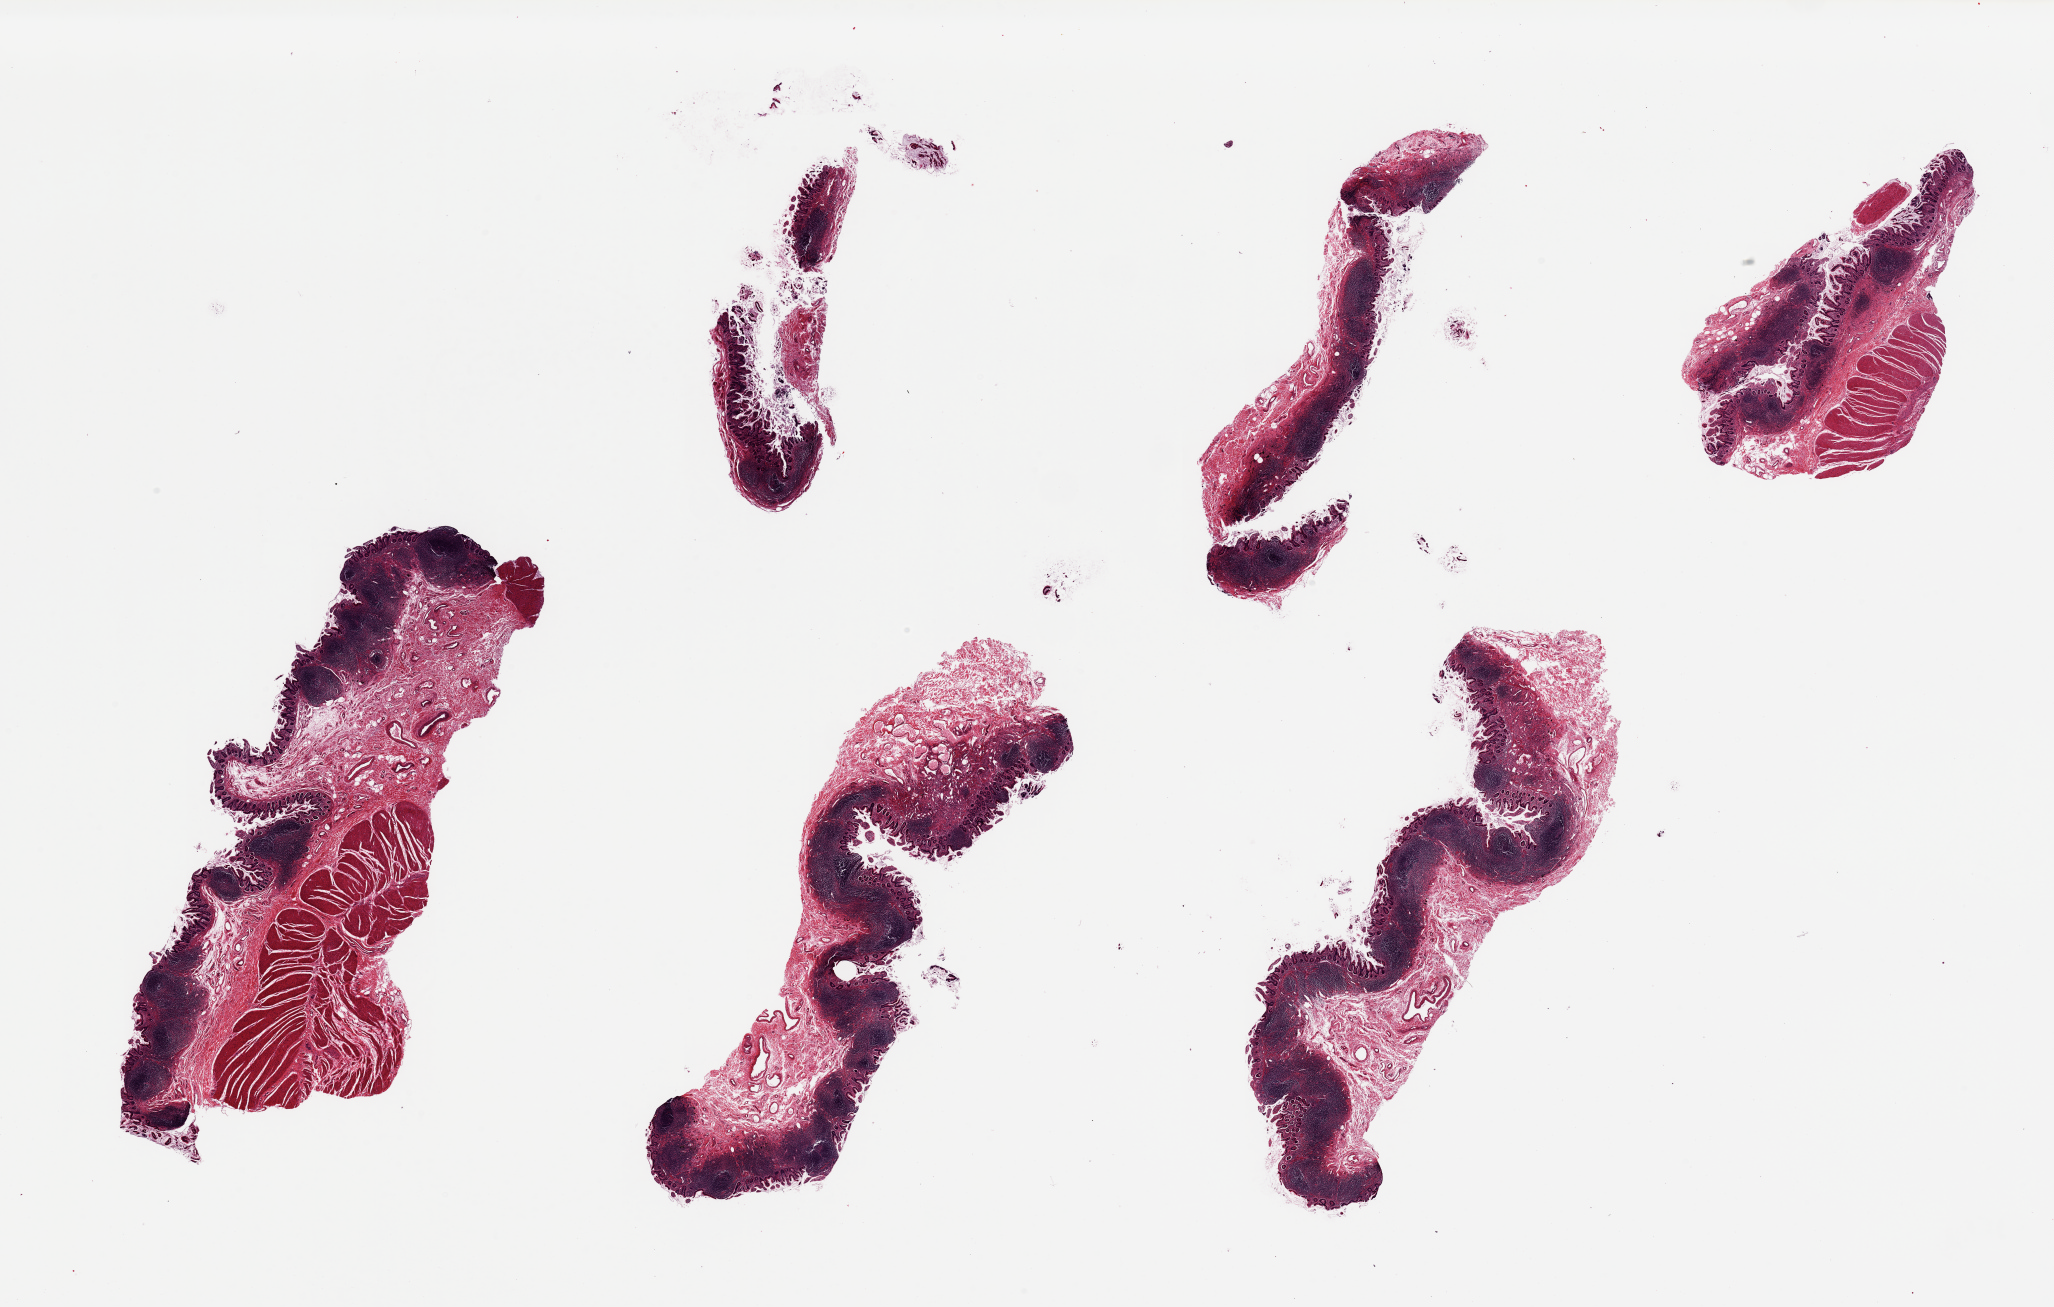
Digitized hematoxylin and eosin (H&E)-stained section — whole scanned area (about 32.5 x 20.7 mm) shown as a low-resolution overview. PAXgene-fixed, paraffin-embedded tissue. Target tissue: ileum. Tissue donor sample. Donor: male.
- reviewer comment on this tissue sample: 6 pieces. Rich lymphoid tissue in all pieces; 2 pieces have muscularis